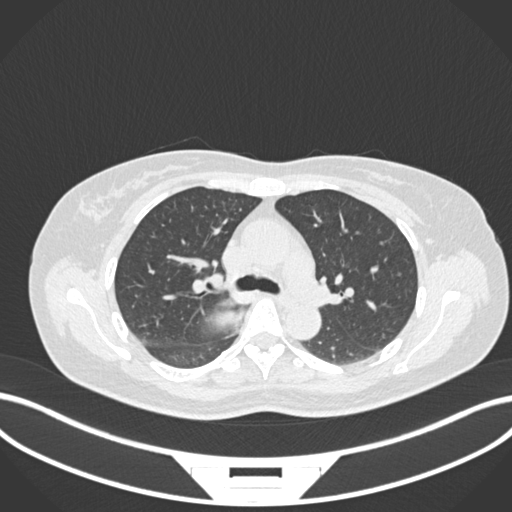
Chest CT, one axial slice; reconstruction kernel B30f; 120 kVp; lung window (W 1500 / L -600 HU); 1 mm slice thickness; 512 × 512 image matrix. Patient: female, 54 years. Case-level facts recorded for this patient, not image findings: clinical TNM (as recorded): T4 N0 M0.
Outlined on this slice (rectangle marked by the reading radiologist):
- lung tumour (recorded histology: adenocarcinoma): bounding box [x1, y1, x2, y2] px = [202, 307, 244, 333]